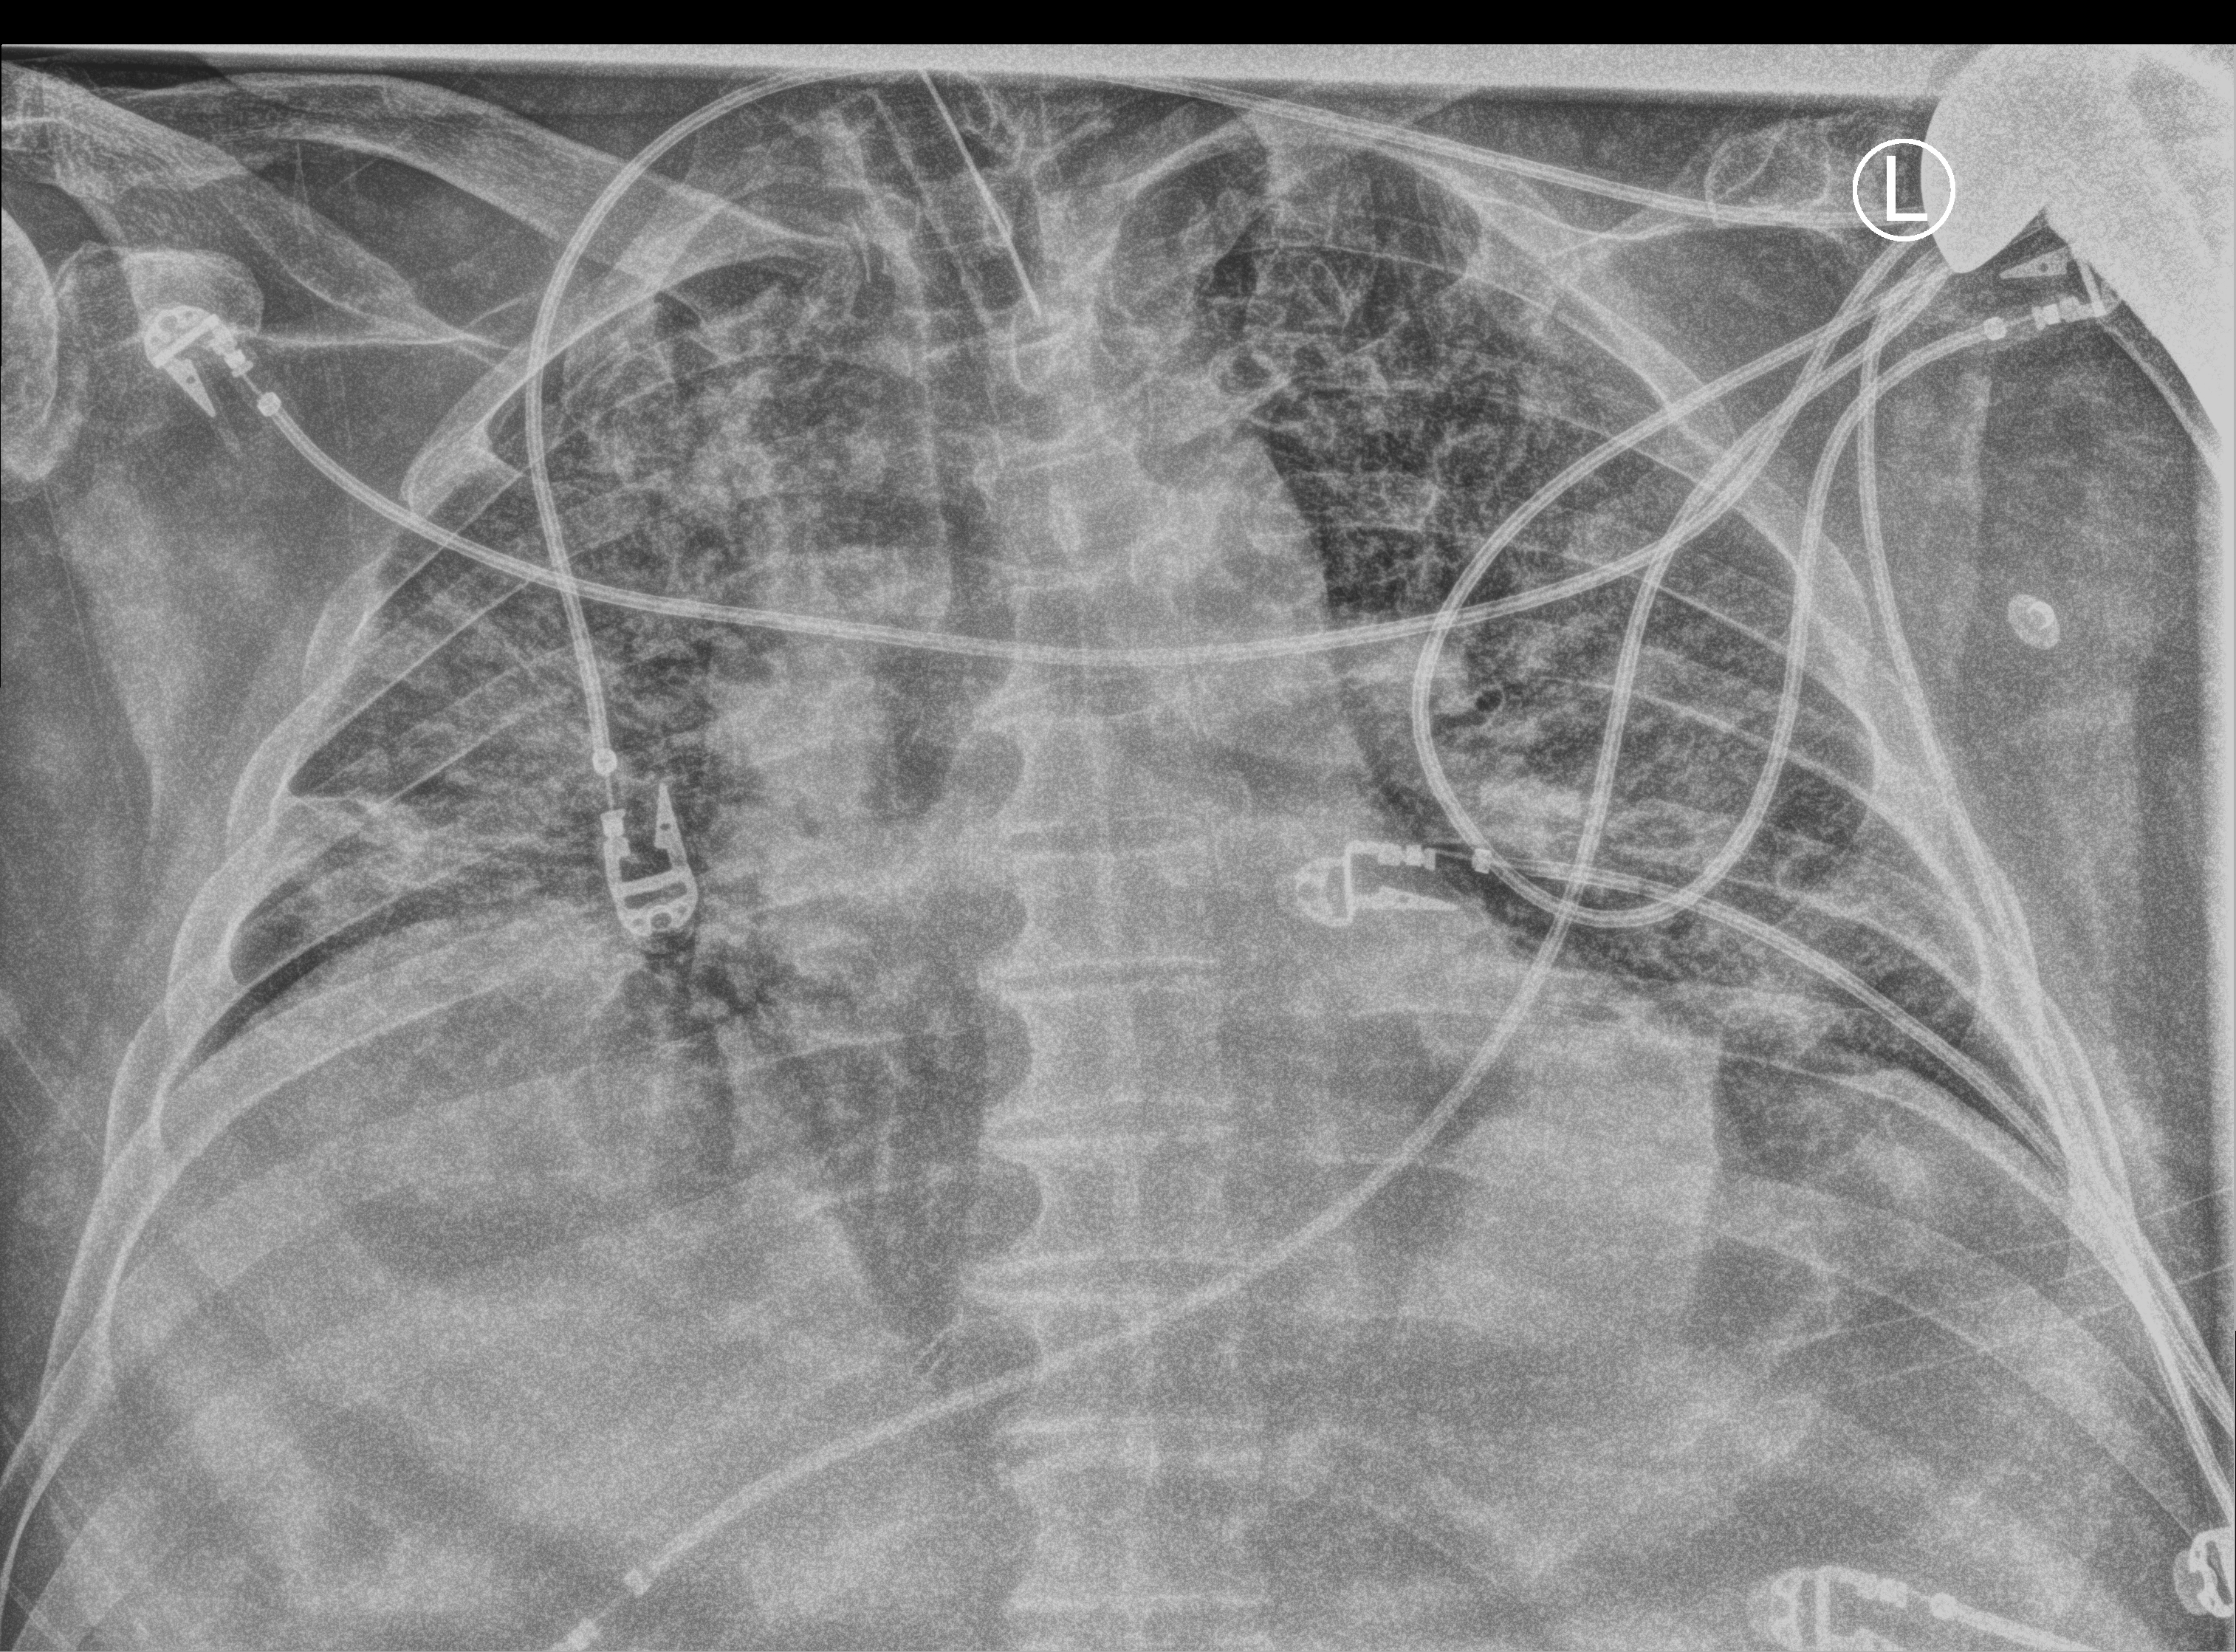
Chest X-ray (portable), anteroposterior (AP) projection. Male patient hospitalised with COVID-19, age 60–74 years.
Admission-level facts for this patient (not findings on this image; timing relative to this image not recorded): mechanically ventilated during this hospital stay: yes; admitted to intensive care during this hospital stay: yes; COPD (admission record): no.